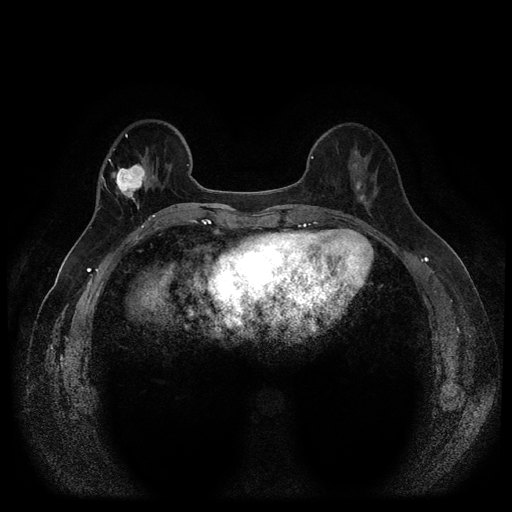
Breast MRI (dynamic contrast-enhanced, multi-phase), one axial slice; position 34 of 116 along the scan axis; dynamic contrast-enhanced series, time point 2 of 5 at this slice position (early post-contrast); 1.5 T; TE 2.6 ms, TR 5.4 ms; 2 mm slice thickness; 512 × 512 image matrix, field of view 340 × 340 mm. Female patient, age 56 years.
Structures marked on this image (semi-automatically segmented with operator editing):
- breast lesion (labelled 'tumour' in the annotation; benign lesions carry a separate 'benign' label): bounding box (x1, y1, x2, y2) in pixels: (110, 157, 150, 203)